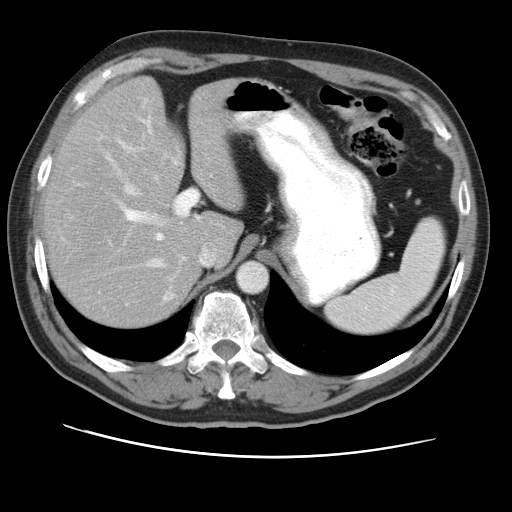
Contrast-enhanced abdominal CT, one axial slice. Position 34 of 49 along the scan axis. 120 kVp. Intravenous contrast given. Soft-tissue window (W 400 / L 40 HU). 5 mm slice thickness. 512 × 512 image matrix, field of view 374 × 374 mm. Male patient, age 59 years. From the clinical record (not read from this slice): diagnosis: colorectal cancer liver metastases, imaged before liver resection; multiple liver metastases: yes; largest metastasis: 6.3 cm; disease in both lobes: yes.
Outlined on this slice (manually delineated by an expert):
- hepatic veins: bounding box [x1, y1, x2, y2] px = [96, 138, 215, 266]
- liver: [45, 80, 239, 327]
- planned liver remnant (the part of the liver to remain after resection): [45, 80, 239, 327]
- portal vein (with intrahepatic branches): [74, 121, 198, 260]